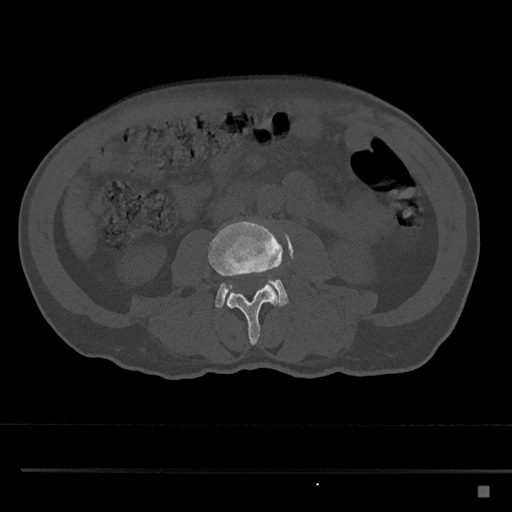
CT including the spine, one axial slice; slice 675 of 797 in the series (ordered by position); reconstruction kernel Br40s/3; bone window (W 1800 / L 400 HU); 0.5 mm slice thickness; 512 × 512 image matrix, field of view 391 × 391 mm. Patient: male, 59 years. From the clinical record (not read from this slice): primary cancer: prostate.
Outlined on this slice (semi-automatic segmentation, software-assisted and operator-edited):
- L3 vertebra: box from (x=208, y=220) to (x=284, y=345) px
- L4 vertebra: (x=215, y=278)–(x=289, y=308)